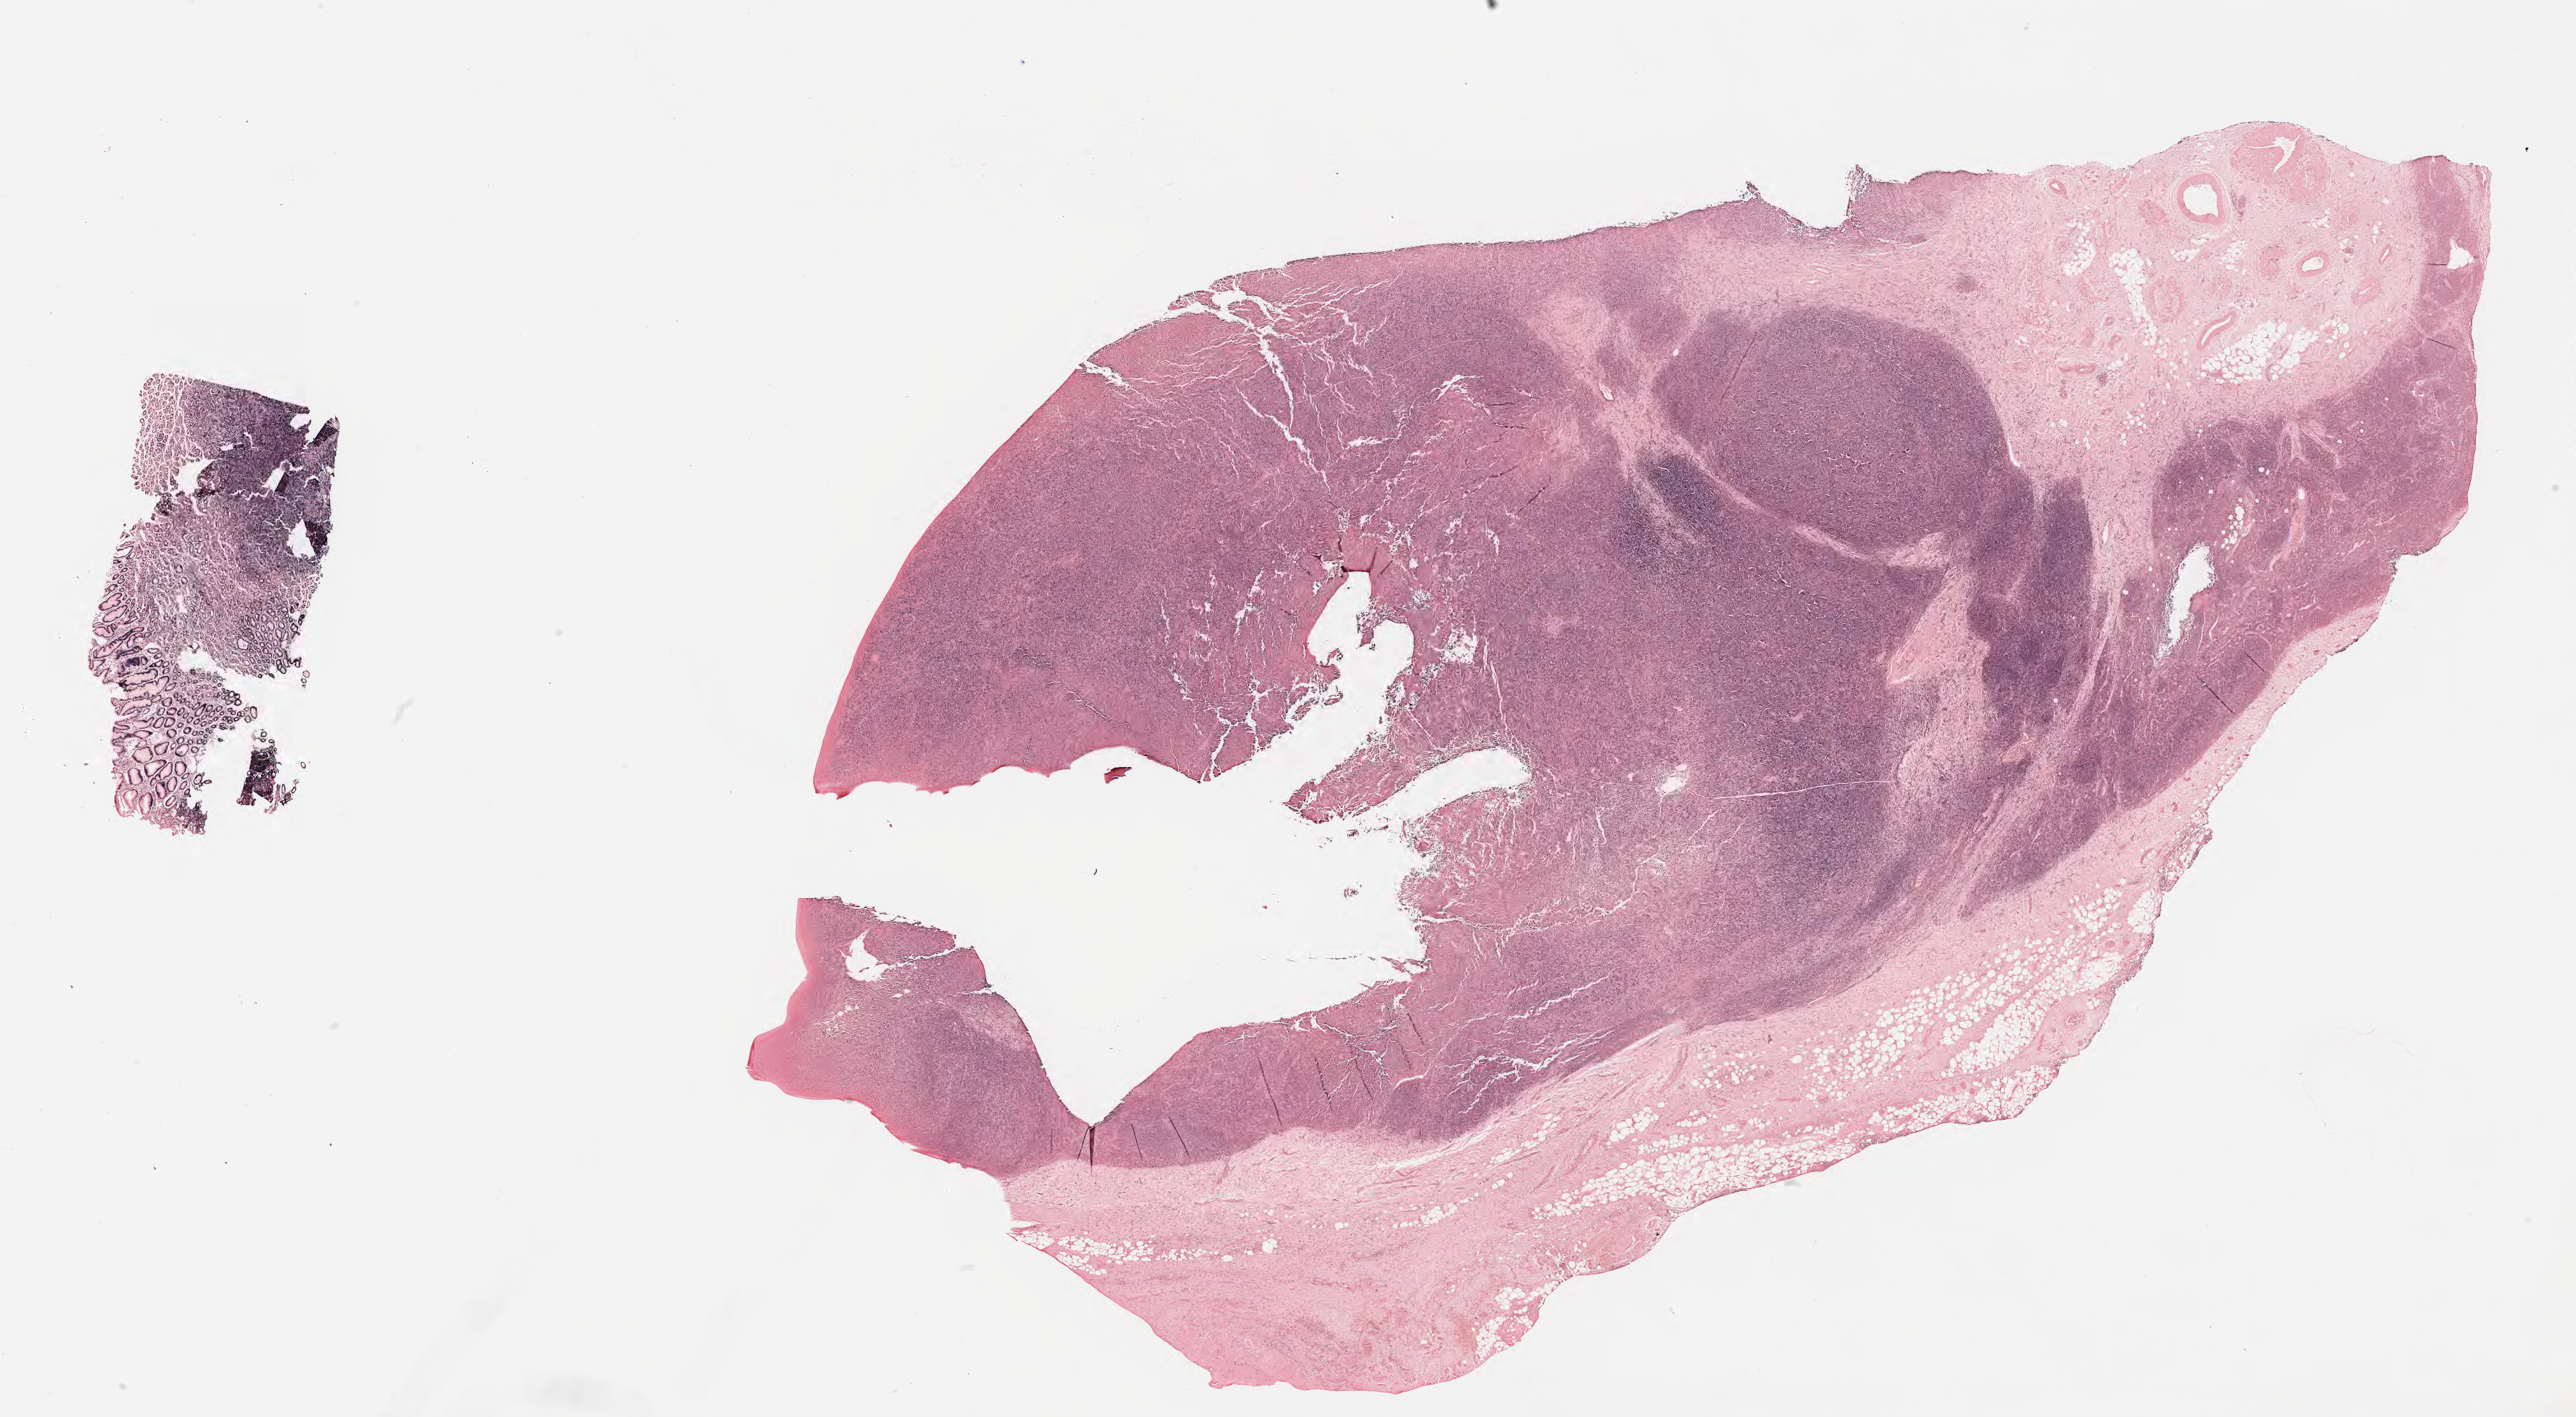
Whole-slide image; stain recorded as Iodonitrotetrazolium — whole scanned area (about 32.7 x 18.0 mm) shown as a low-resolution overview; tumor tissue; site: lymph node. Patient: male, age 60 years.
• histologic diagnosis: Diffuse large B-cell lymphoma, NOS